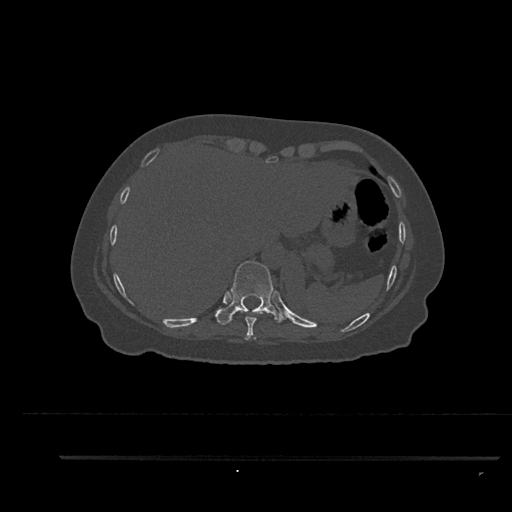
CT including the spine, one axial slice. Position 382 of 797 along the scan axis. 120 kVp. Bone window (W 1800 / L 400 HU). 0.5 mm slice thickness. 512 × 512 image matrix, field of view 408 × 408 mm. Patient: female, 44 years. From the clinical record (not read from this slice): primary cancer: renal; vertebrae with lytic lesions (as recorded): L1.
Outlined on this slice (semi-automatic segmentation, software-assisted and operator-edited):
- T10 vertebra: bounding box <216,261,284,325> (left, top, right, bottom; pixels)
- T9 vertebra: <239,308,263,340>